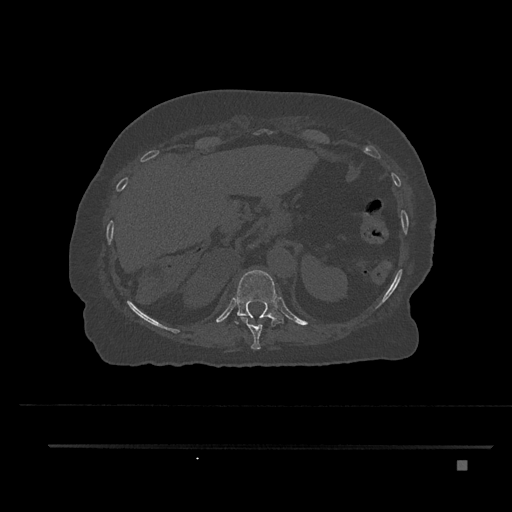
CT including the spine, one axial slice. Position 326 of 797 along the scan axis. Reconstruction kernel Br40s/3. 120 kVp. Bone window (W 1800 / L 400 HU). 0.5 mm slice thickness. 512 × 512 image matrix. Patient: female, 76 years. Case-level facts recorded for this patient, not image findings: primary cancer: lung; vertebrae with lytic lesions (as recorded): T11, L3.
Outlined on this slice (semi-automatically segmented with operator editing):
- T10 vertebra: bounding box <240,317,263,350> (left, top, right, bottom; pixels)
- T11 vertebra: <236,270,284,327>